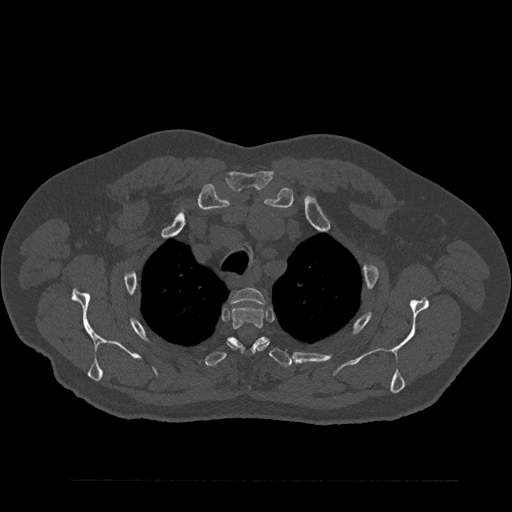
CT including the spine, one axial slice. Position 675 of 797 along the scan axis. Reconstruction kernel Br40s/3. Bone window (W 1800 / L 400 HU). 0.5 mm slice thickness. 512 × 512 image matrix, field of view 430 × 430 mm. Male patient, age 61 years. Case-level facts recorded for this patient, not image findings: primary cancer: prostate.
Annotated regions visible in this slice (semi-automatically segmented with operator editing):
- T2 vertebra: box from (x=231, y=288) to (x=266, y=304) px
- T3 vertebra: (x=231, y=306)–(x=269, y=353)
- T4 vertebra: (x=205, y=336)–(x=292, y=367)